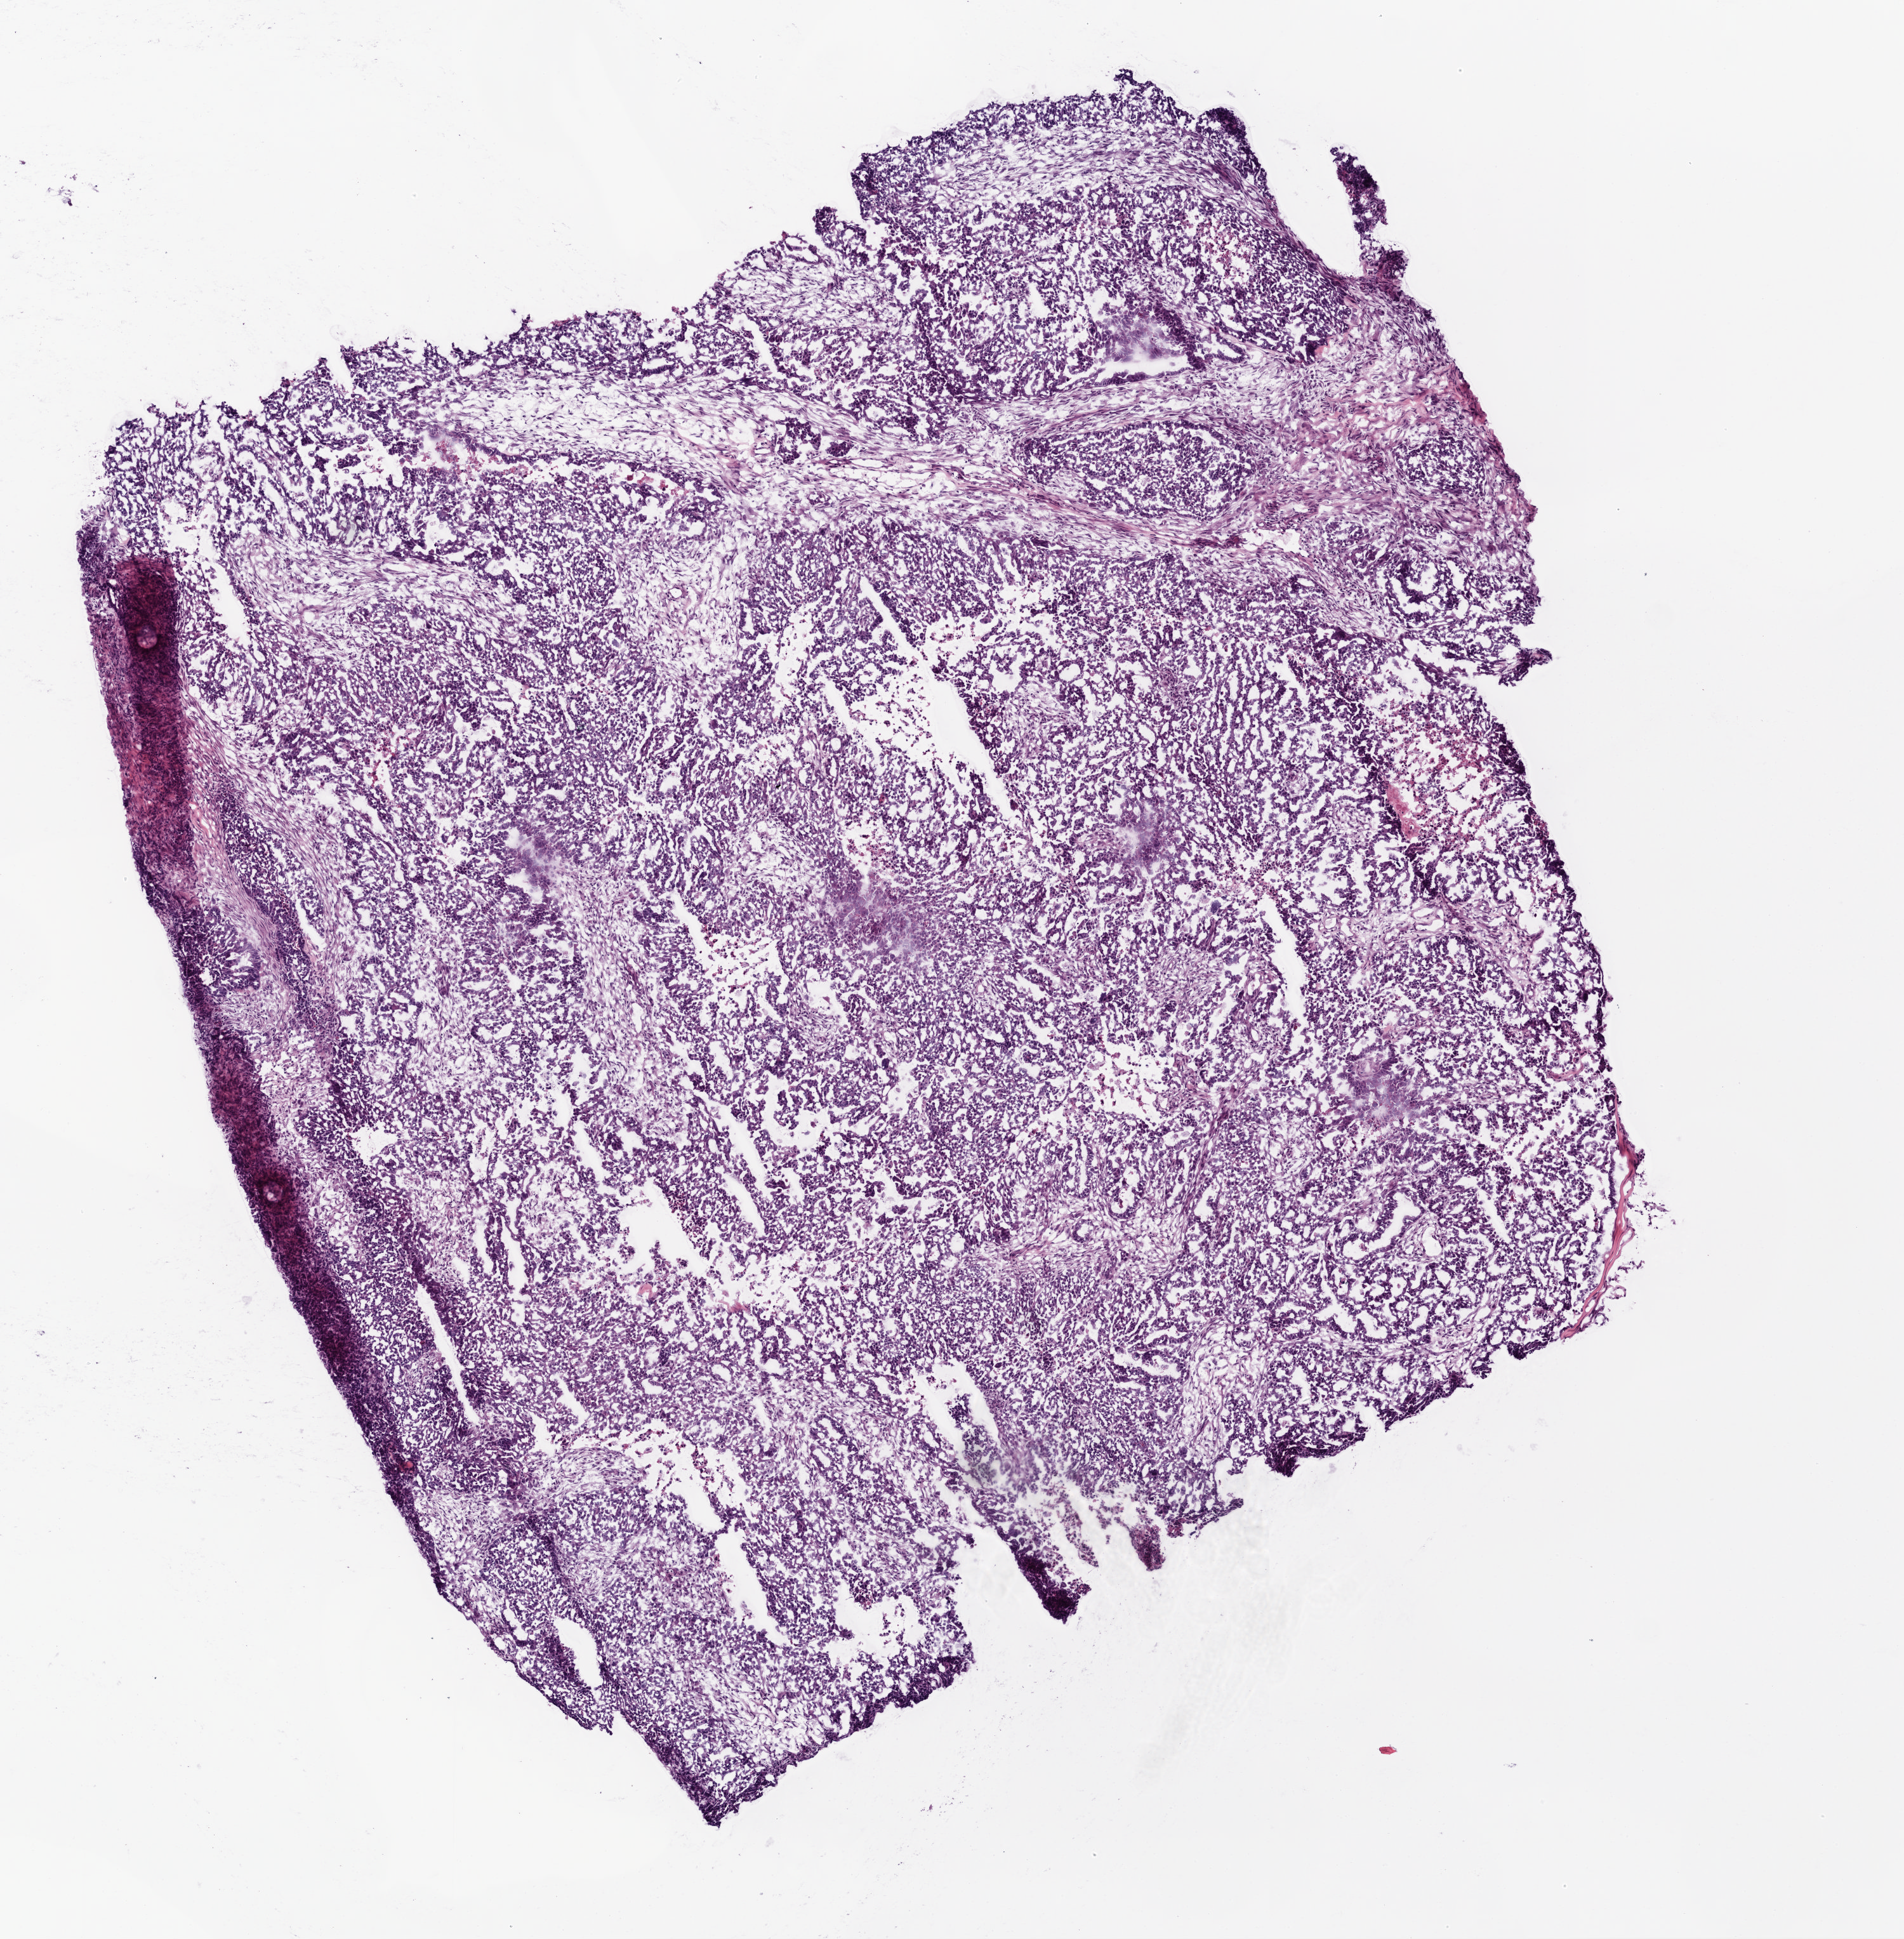
H&E whole-slide image — low-resolution overview of the scanned area, about 6.0 x 6.1 mm (acquisition: 20x scan); frozen section from the top of the tissue portion; ovary, primary tumour sample. Female patient; age at initial diagnosis 66 years. Histologic grade: G3 (poorly differentiated). Composition of this section per pathologist review: tumour cells 89%, tumour nuclei 90%, normal cells 0%, stromal cells 10%, necrosis 1%.
Histologic diagnosis: Serous cystadenocarcinoma, NOS. Laterality: bilateral. FIGO stage: IIIC.